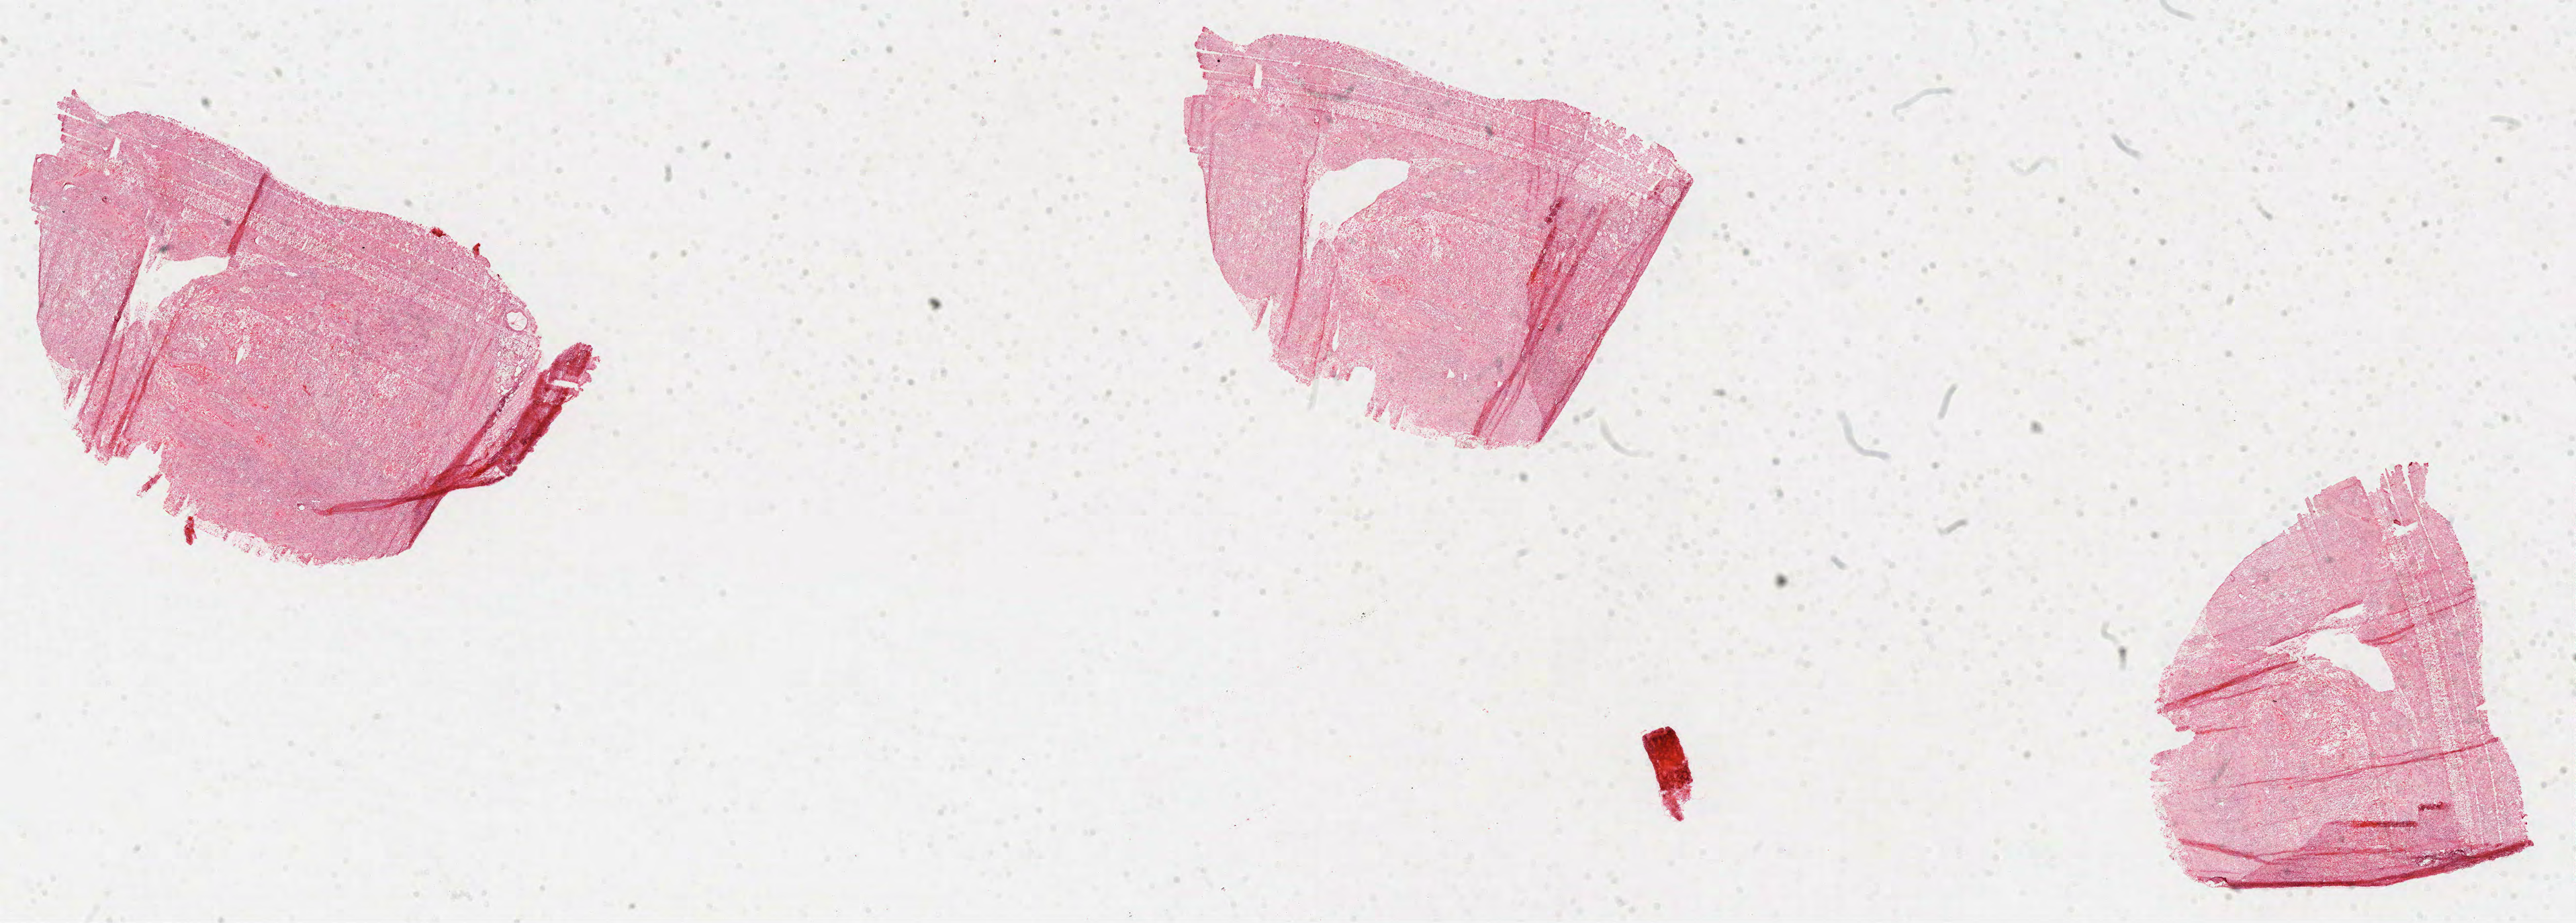
Whole-slide histology image, Hematoxylin and eosin (H&E) stained — whole scanned area (about 30.9 x 11.1 mm) shown as a low-resolution overview. Formalin-fixed paraffin-embedded (FFPE) diagnostic section. Sample: primary tumour, head and neck. Male patient; age at initial diagnosis 61 years. Histologic grade: G2 (moderately differentiated).
Histologic diagnosis: Squamous cell carcinoma, NOS (larynx, NOS). AJCC pathologic stage: IVA.